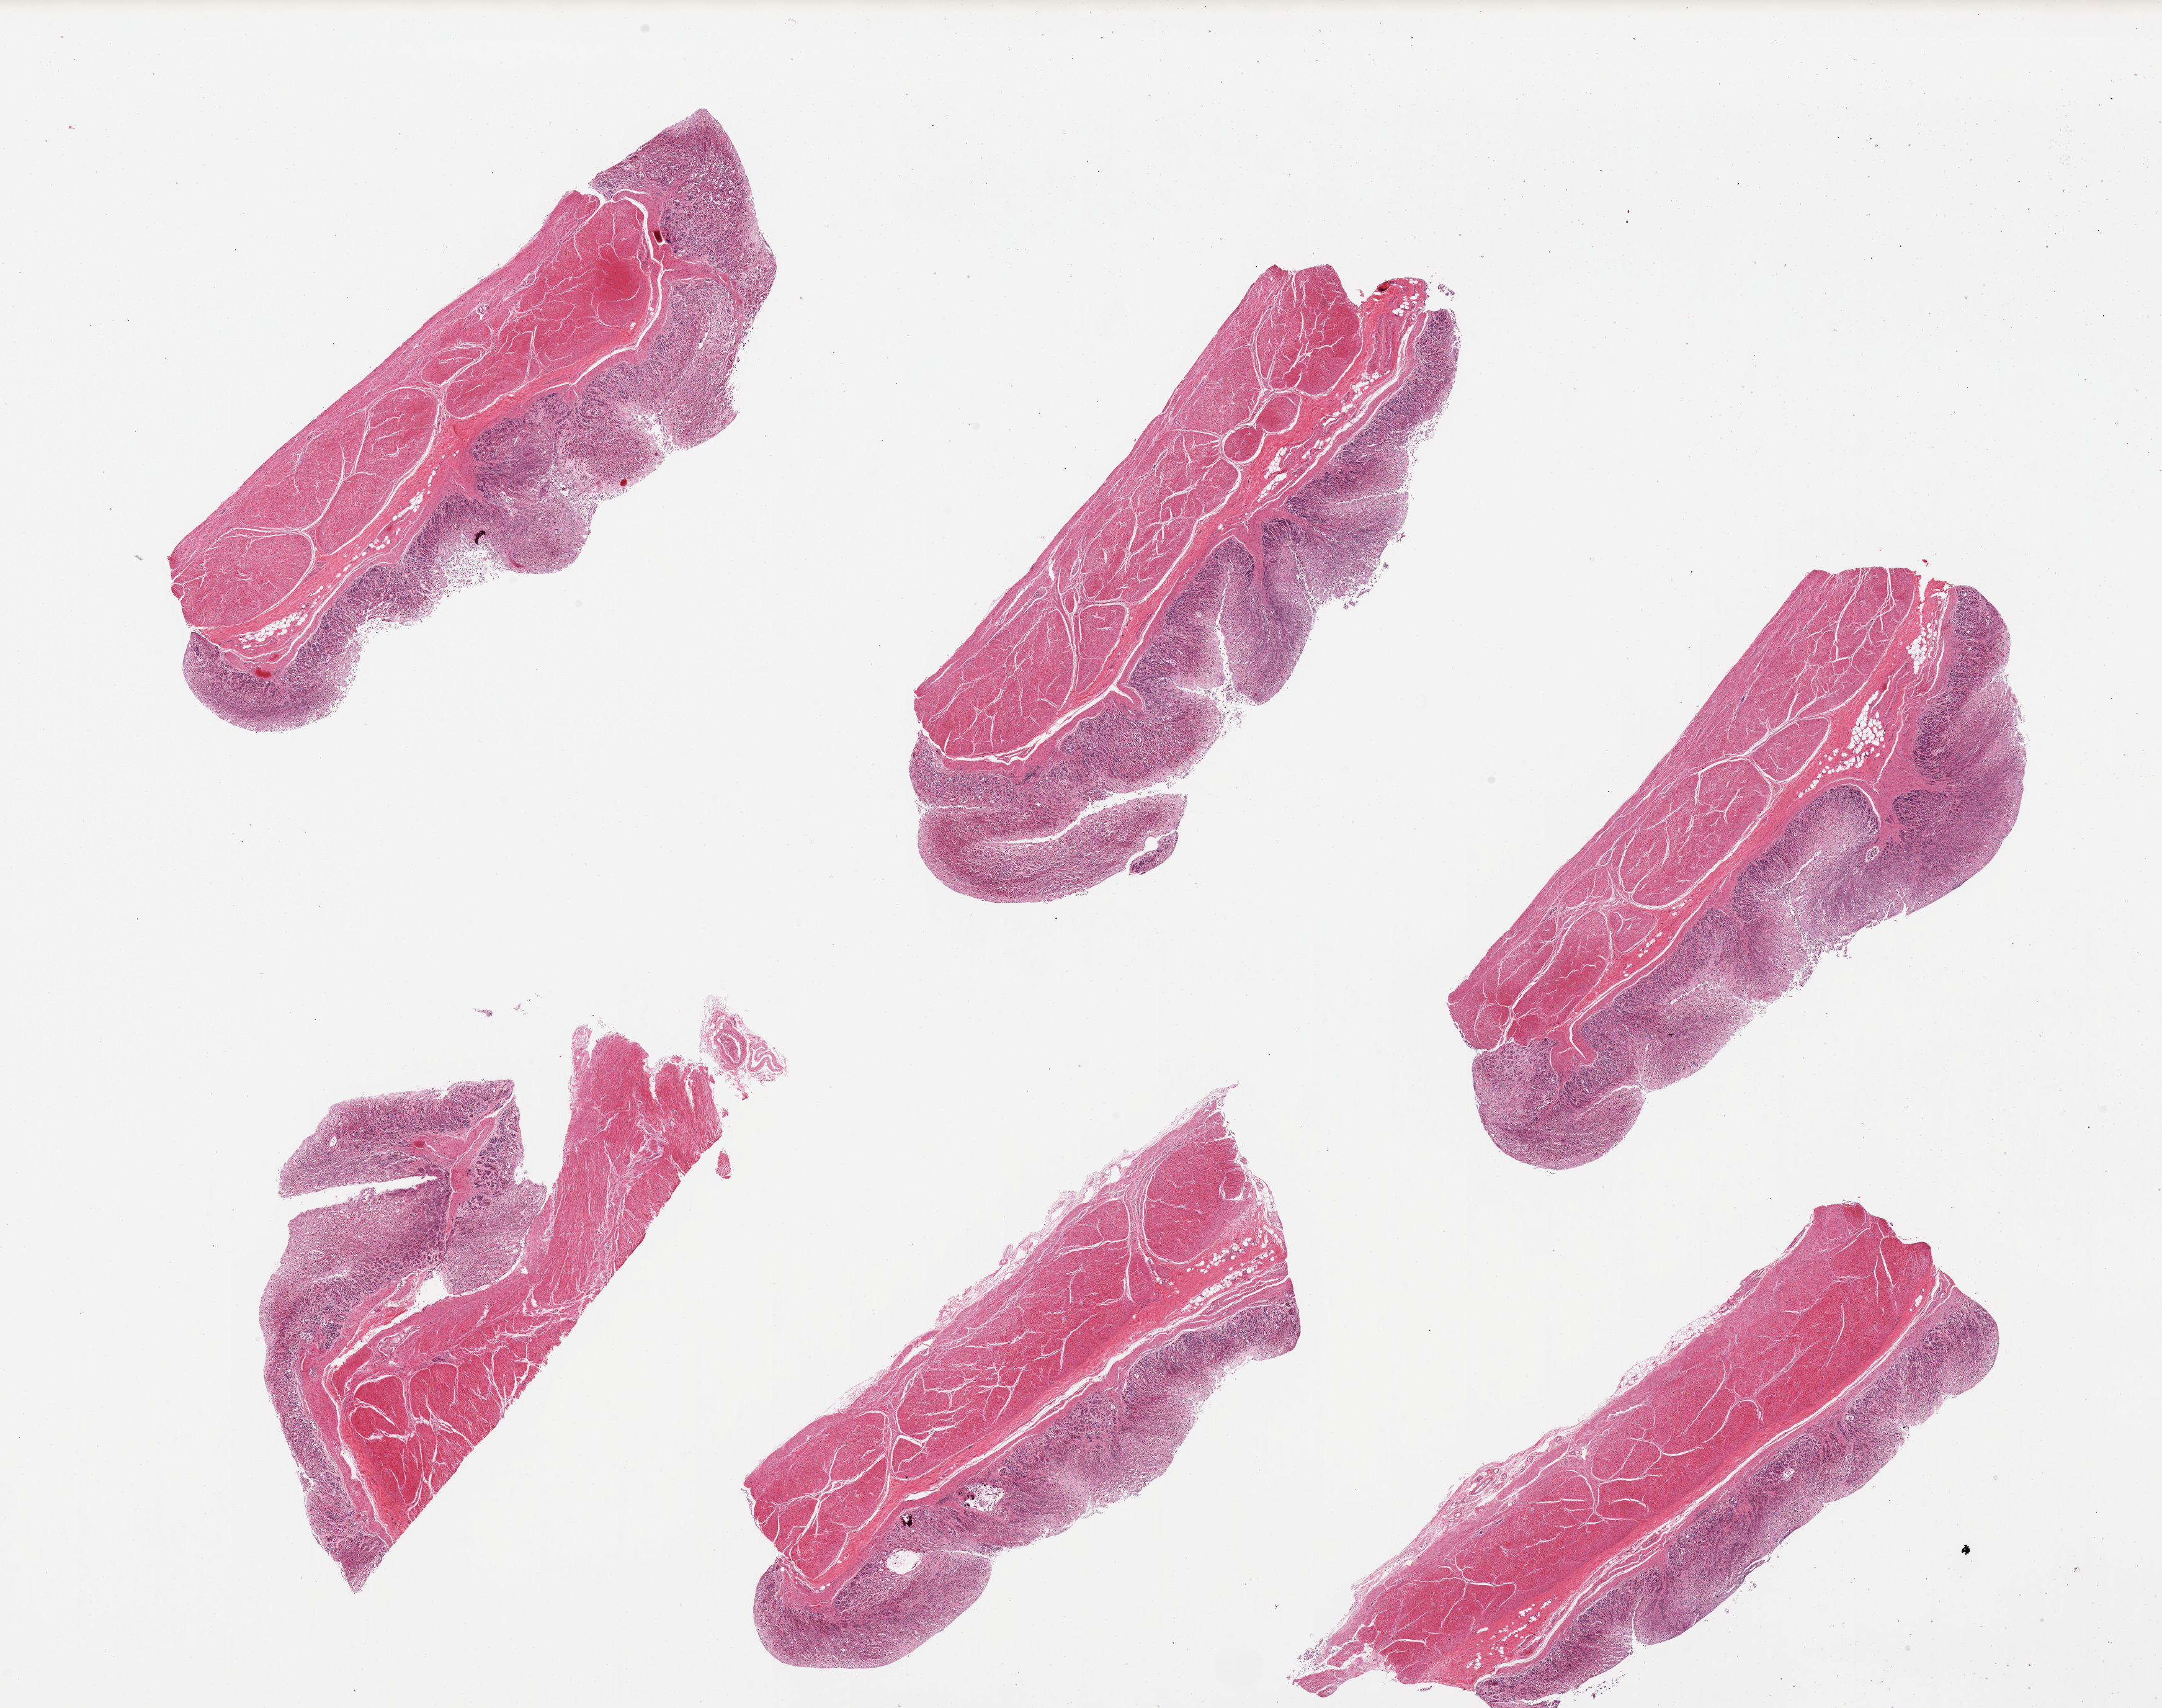
Digitized haematoxylin and eosin-stained section — a low-resolution overview of the entire scanned area, about 27.6 x 21.8 mm; PAXgene-fixed paraffin-embedded (PFPE) section; target tissue: stomach; donor tissue sample. Donor: male.
Reviewer comment on this tissue sample: 6 pieces.